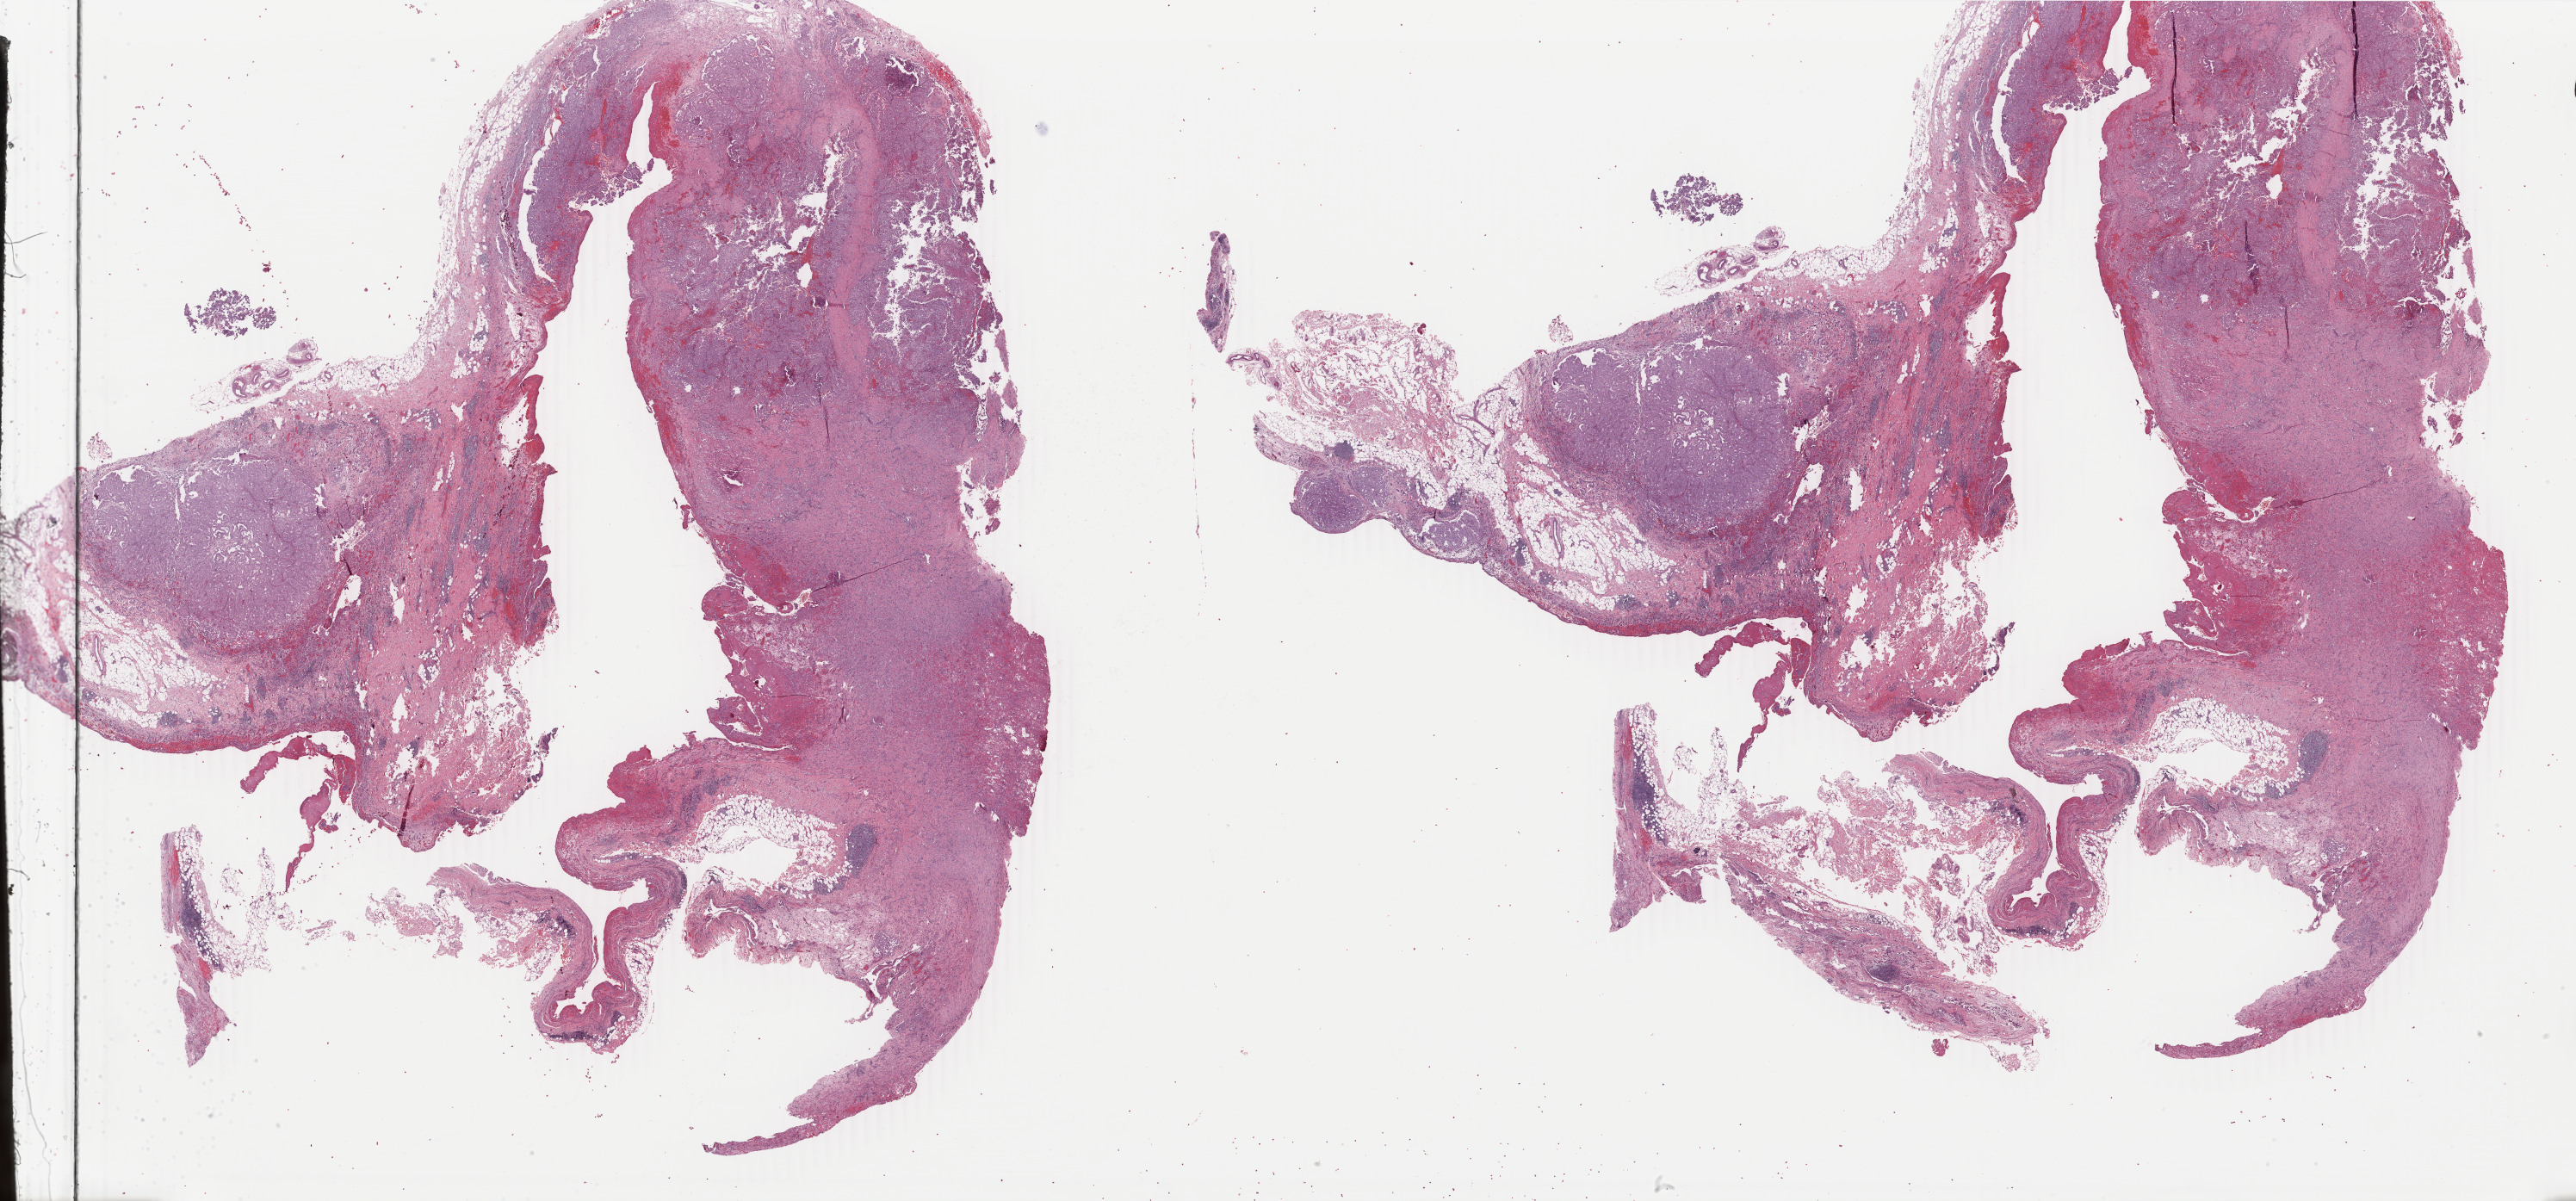
Digitized Hematoxylin and eosin (H&E) stained tissue section (whole slide) — a low-resolution overview of the entire scanned area, about 47.6 x 22.2 mm, formalin-fixed paraffin-embedded (FFPE) diagnostic section, primary tumour sample from the mesothelium. Male patient; age at initial diagnosis 60 years.
* AJCC pathologic stage: IV (6th edition)
* laterality: left
* histologic diagnosis: Mesothelioma, malignant (pleura, NOS)